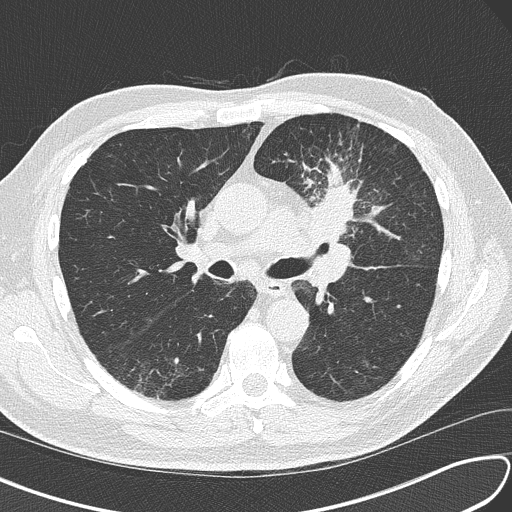
Chest CT (low-dose screening protocol), one axial image, third annual screen, lung window (W 1500 / L -600 HU), 2 mm slice thickness, lung (sharp) reconstruction kernel (B50f), slice 64 of 156 in the series, 512 × 512 image matrix, field of view 340 × 340 mm. Male participant, aged 67 years at enrolment.
Expert reader's lesion annotation, bounding box <295,162,395,253> (left, top, right, bottom; pixels). Screening reader's record for this exam (one nodule recorded; not confirmed to be the boxed lesion): non-calcified nodule or mass ≥4 mm, left upper lobe, 30 × 23 mm, soft tissue attenuation, pre-existing on the prior screen: no. Later outcome: lung cancer diagnosed 41 days after this screen — small cell carcinoma, NOS, left upper lobe, stage IV (AJCC 6th edition), 30 mm at pathology.